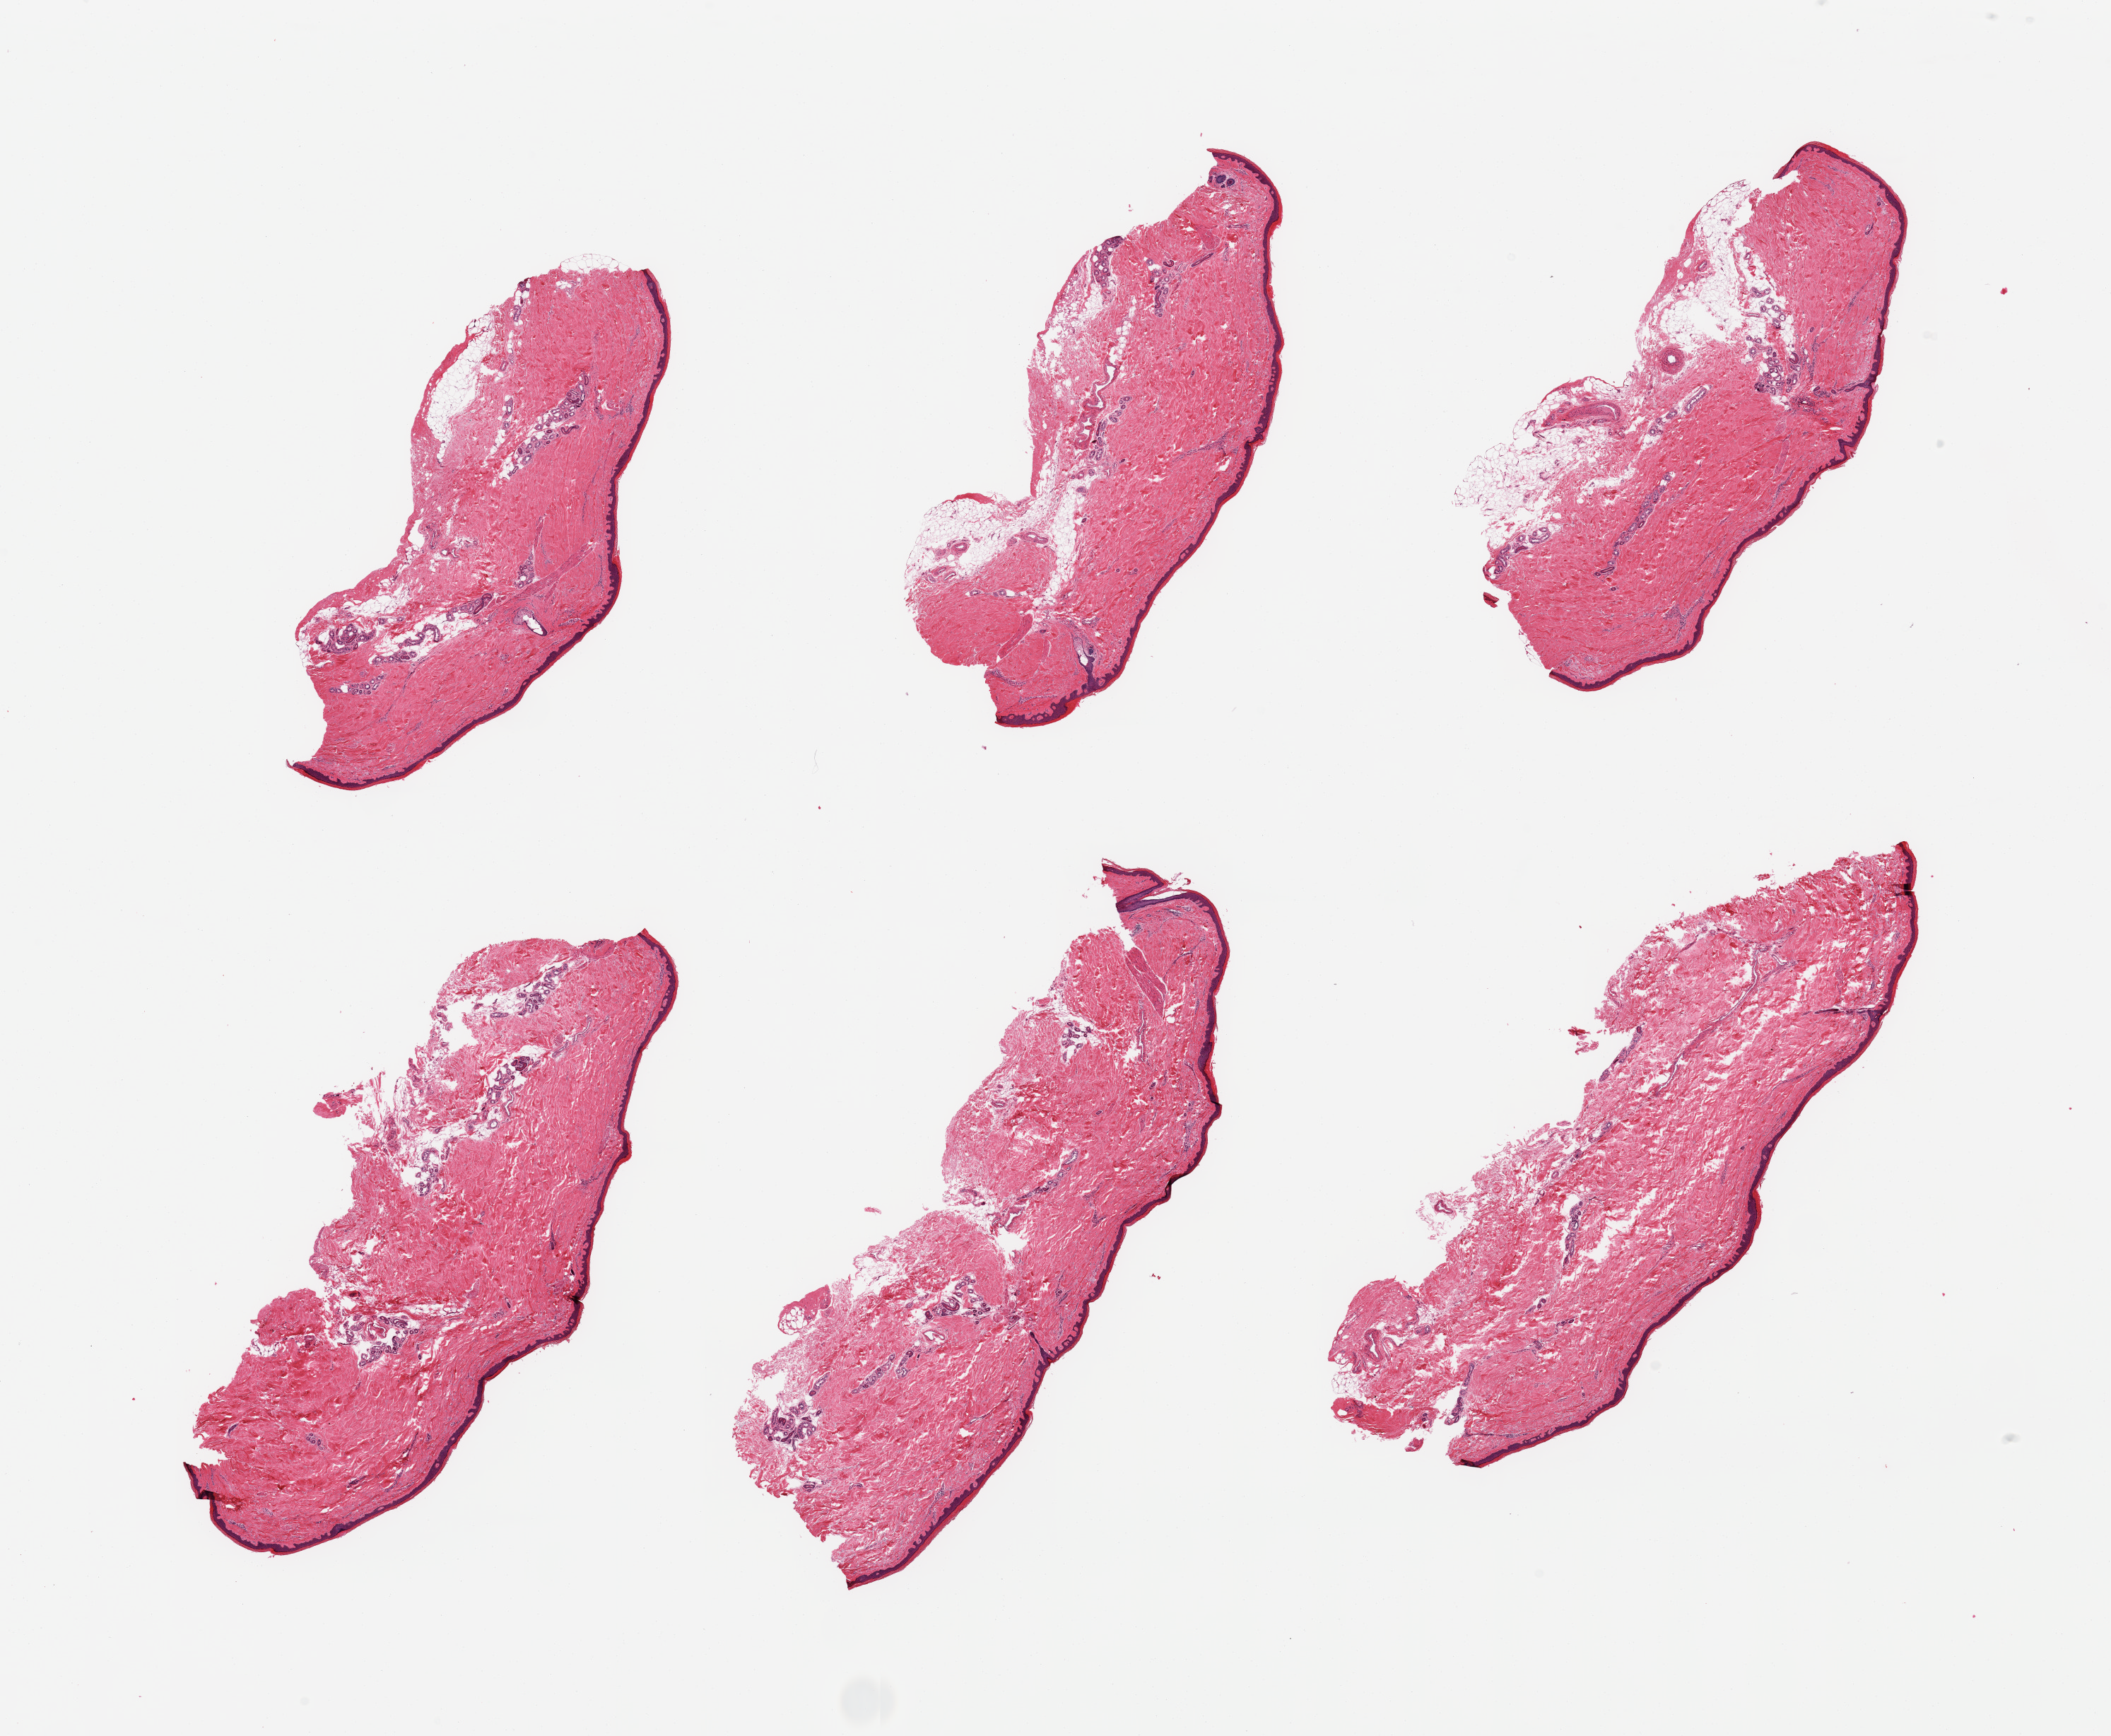
H&E whole-slide image, low-resolution overview of the scanned area, about 23.6 x 19.4 mm (acquisition: 20x scan), PAXgene-fixed, paraffin-embedded tissue, sampled site (target tissue): skin of lower leg, tissue donor sample. Male donor.
Reviewer comment on this tissue sample: 6 pieces; includes from 5-15% fat; epidermis measures ~35-40 microns.